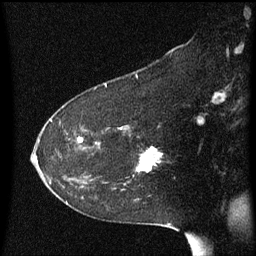
Breast MRI (dynamic contrast-enhanced), one sagittal slice; position 37 of 60 along the scan axis; dynamic contrast-enhanced series, image 2 of 3 at this slice position (ordered by acquisition); 1.5 T; TE 4.2 ms, TR 8.4 ms; 256 × 256 image matrix, field of view 200 × 200 mm. Patient: female, 54 years. From the clinical record (not read from this slice): setting: breast cancer imaged before/during neoadjuvant chemotherapy; receptor status: HR-positive, HER2-negative.
Outlined on this slice (semi-automatically segmented with operator editing):
- analysis volume of interest (the breast-tissue region the enhancement analysis was run in; not a lesion): bounding box (x1, y1, x2, y2) in pixels: (125, 132, 165, 179)
- tumour enhancement mask (voxels above the 70 % enhancement threshold inside the analysis volume of interest): (137, 148, 160, 173)